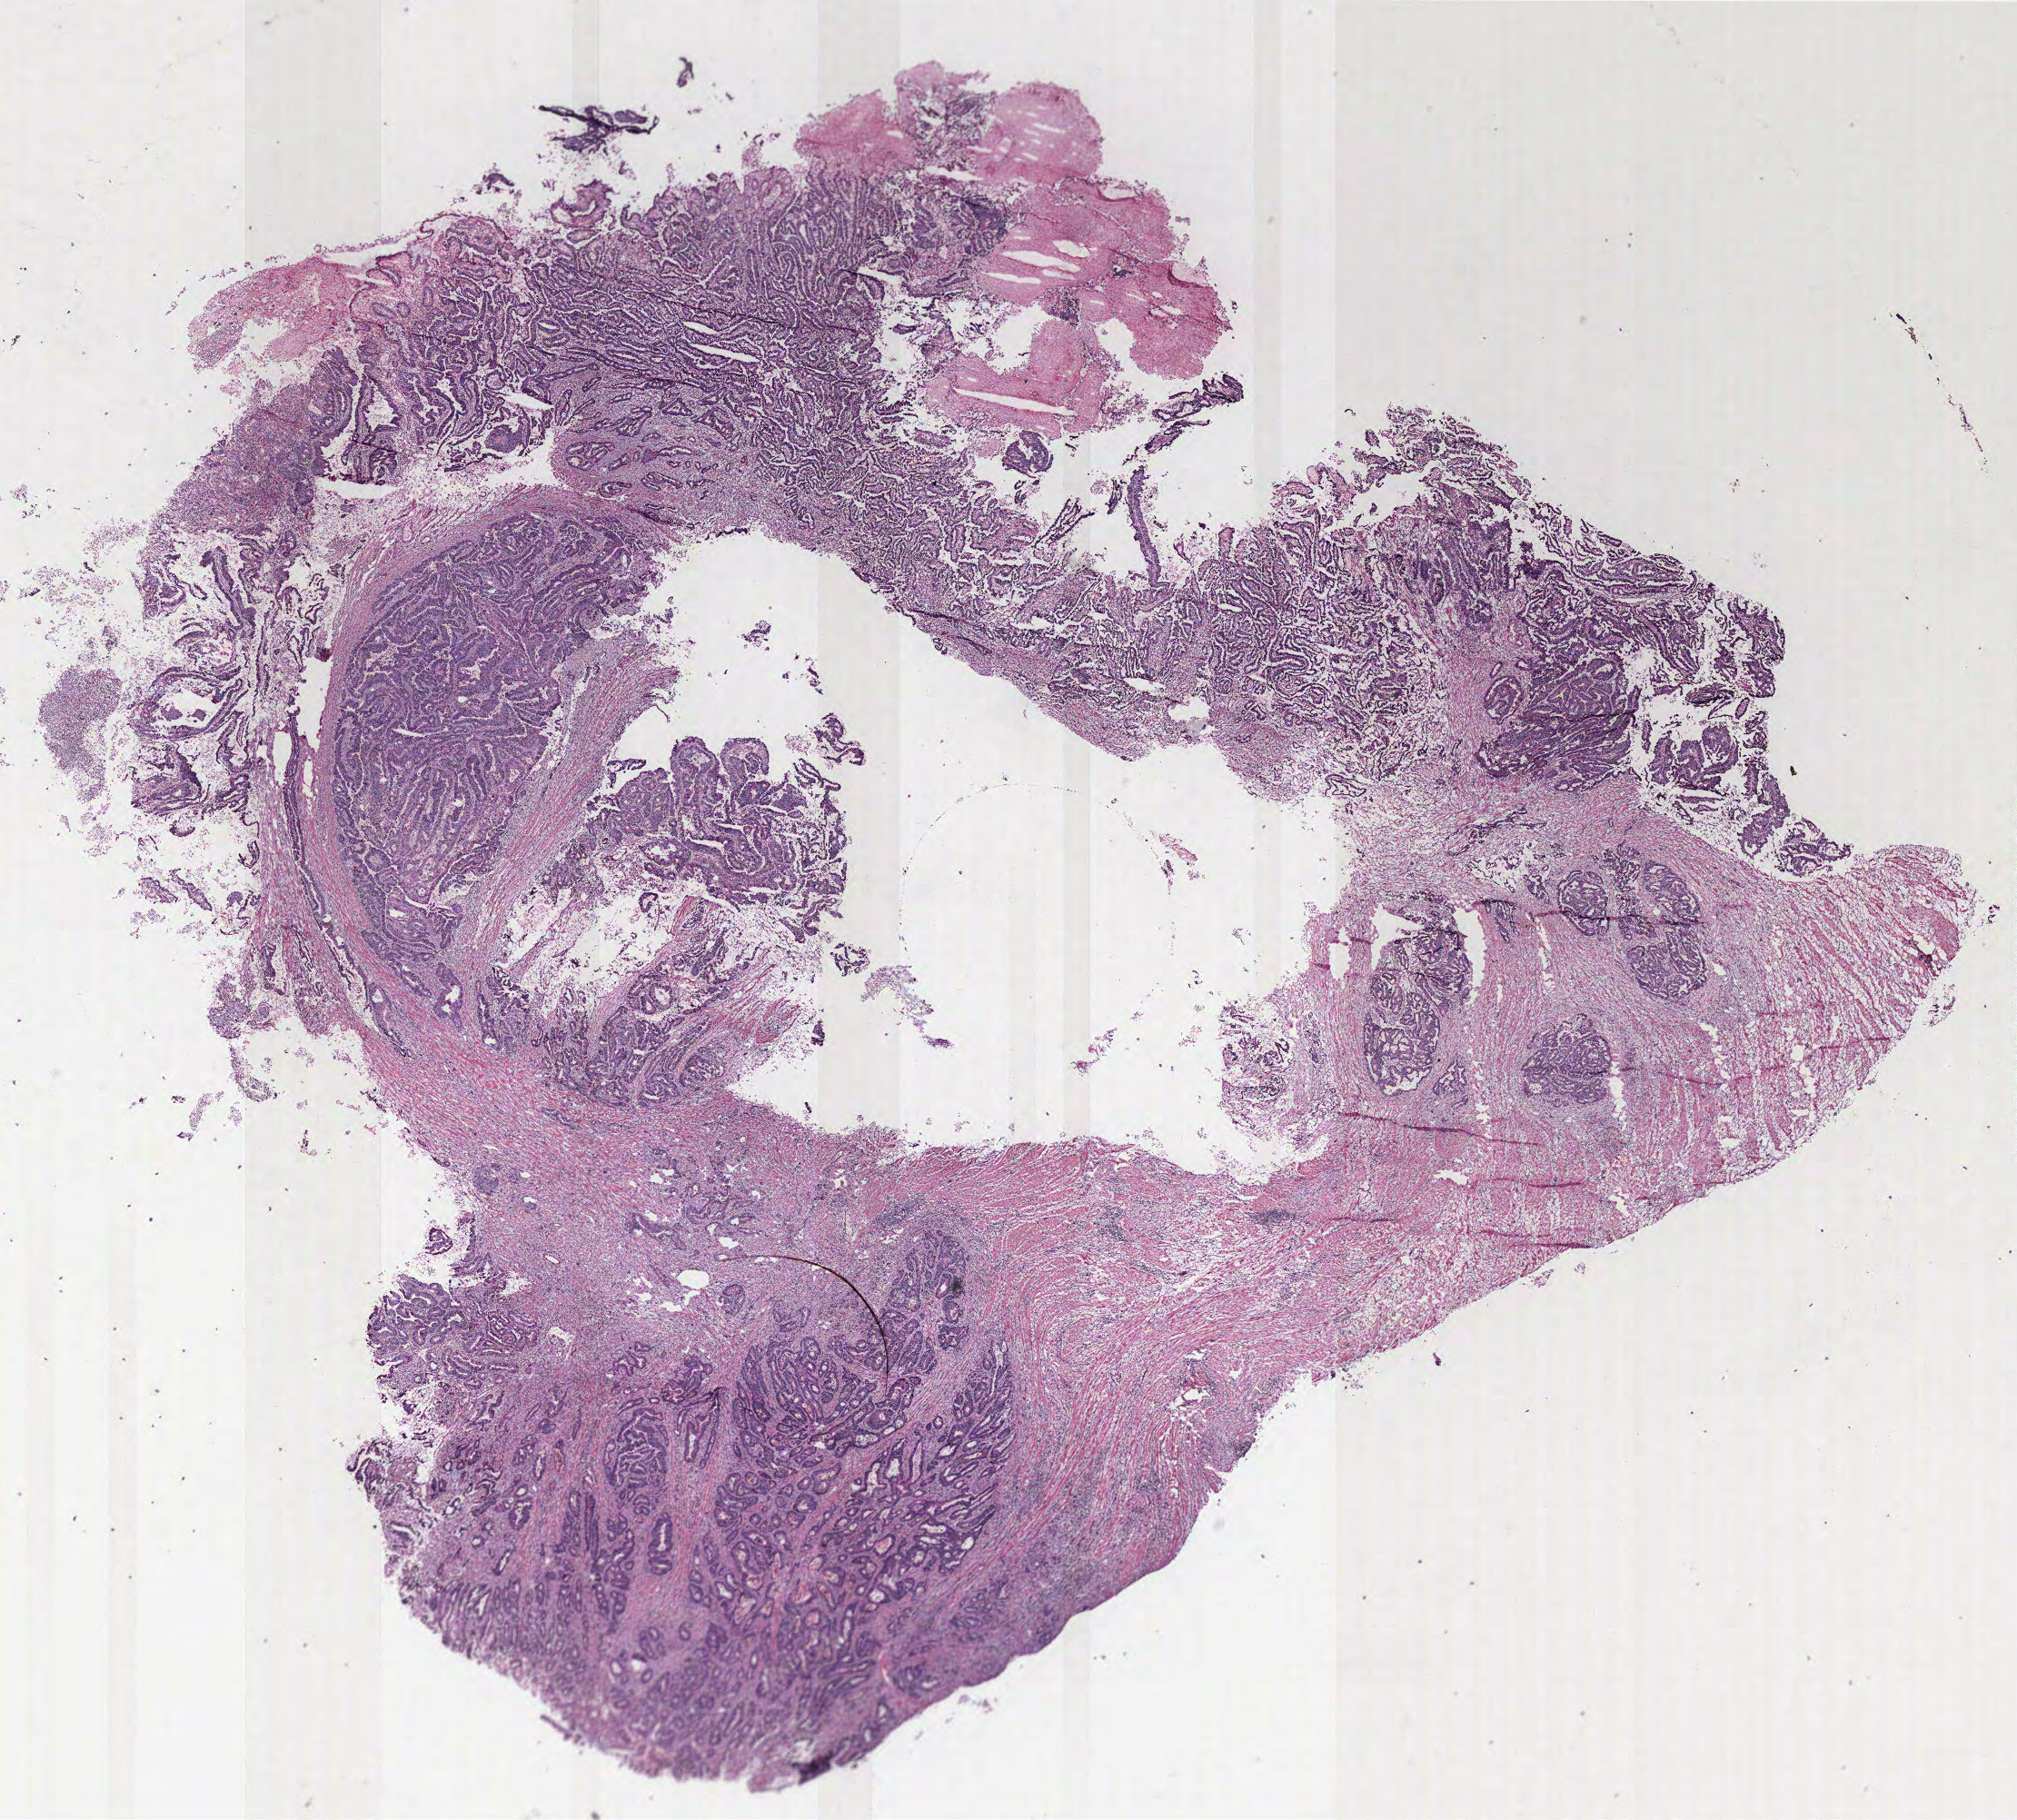
Hematoxylin and eosin (H&E) stained whole-slide image, low-resolution overview of the scanned area, about 17.8 x 16.0 mm, colon, normal (non-tumour) tissue. 59-year-old male patient.
* this section: normal (non-tumour) tissue from the same patient
* patient diagnosis: Adenocarcinoma, NOS